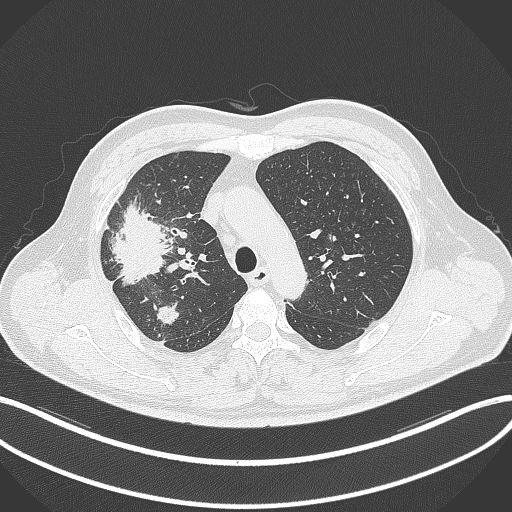
Chest CT, one axial slice; position 246 of 348 along the scan axis; reconstruction kernel B70f; lung window (W 1500 / L -600 HU); 1 mm slice thickness; 512 × 512 image matrix, field of view 400 × 400 mm. Patient: male, 55 years. From the clinical record (not read from this slice): clinical TNM (as recorded): T3 N2 M1.
Annotated regions visible in this slice (bounding box drawn by a radiologist):
- lung tumour (recorded histology: adenocarcinoma): box from (x=107, y=199) to (x=171, y=289) px